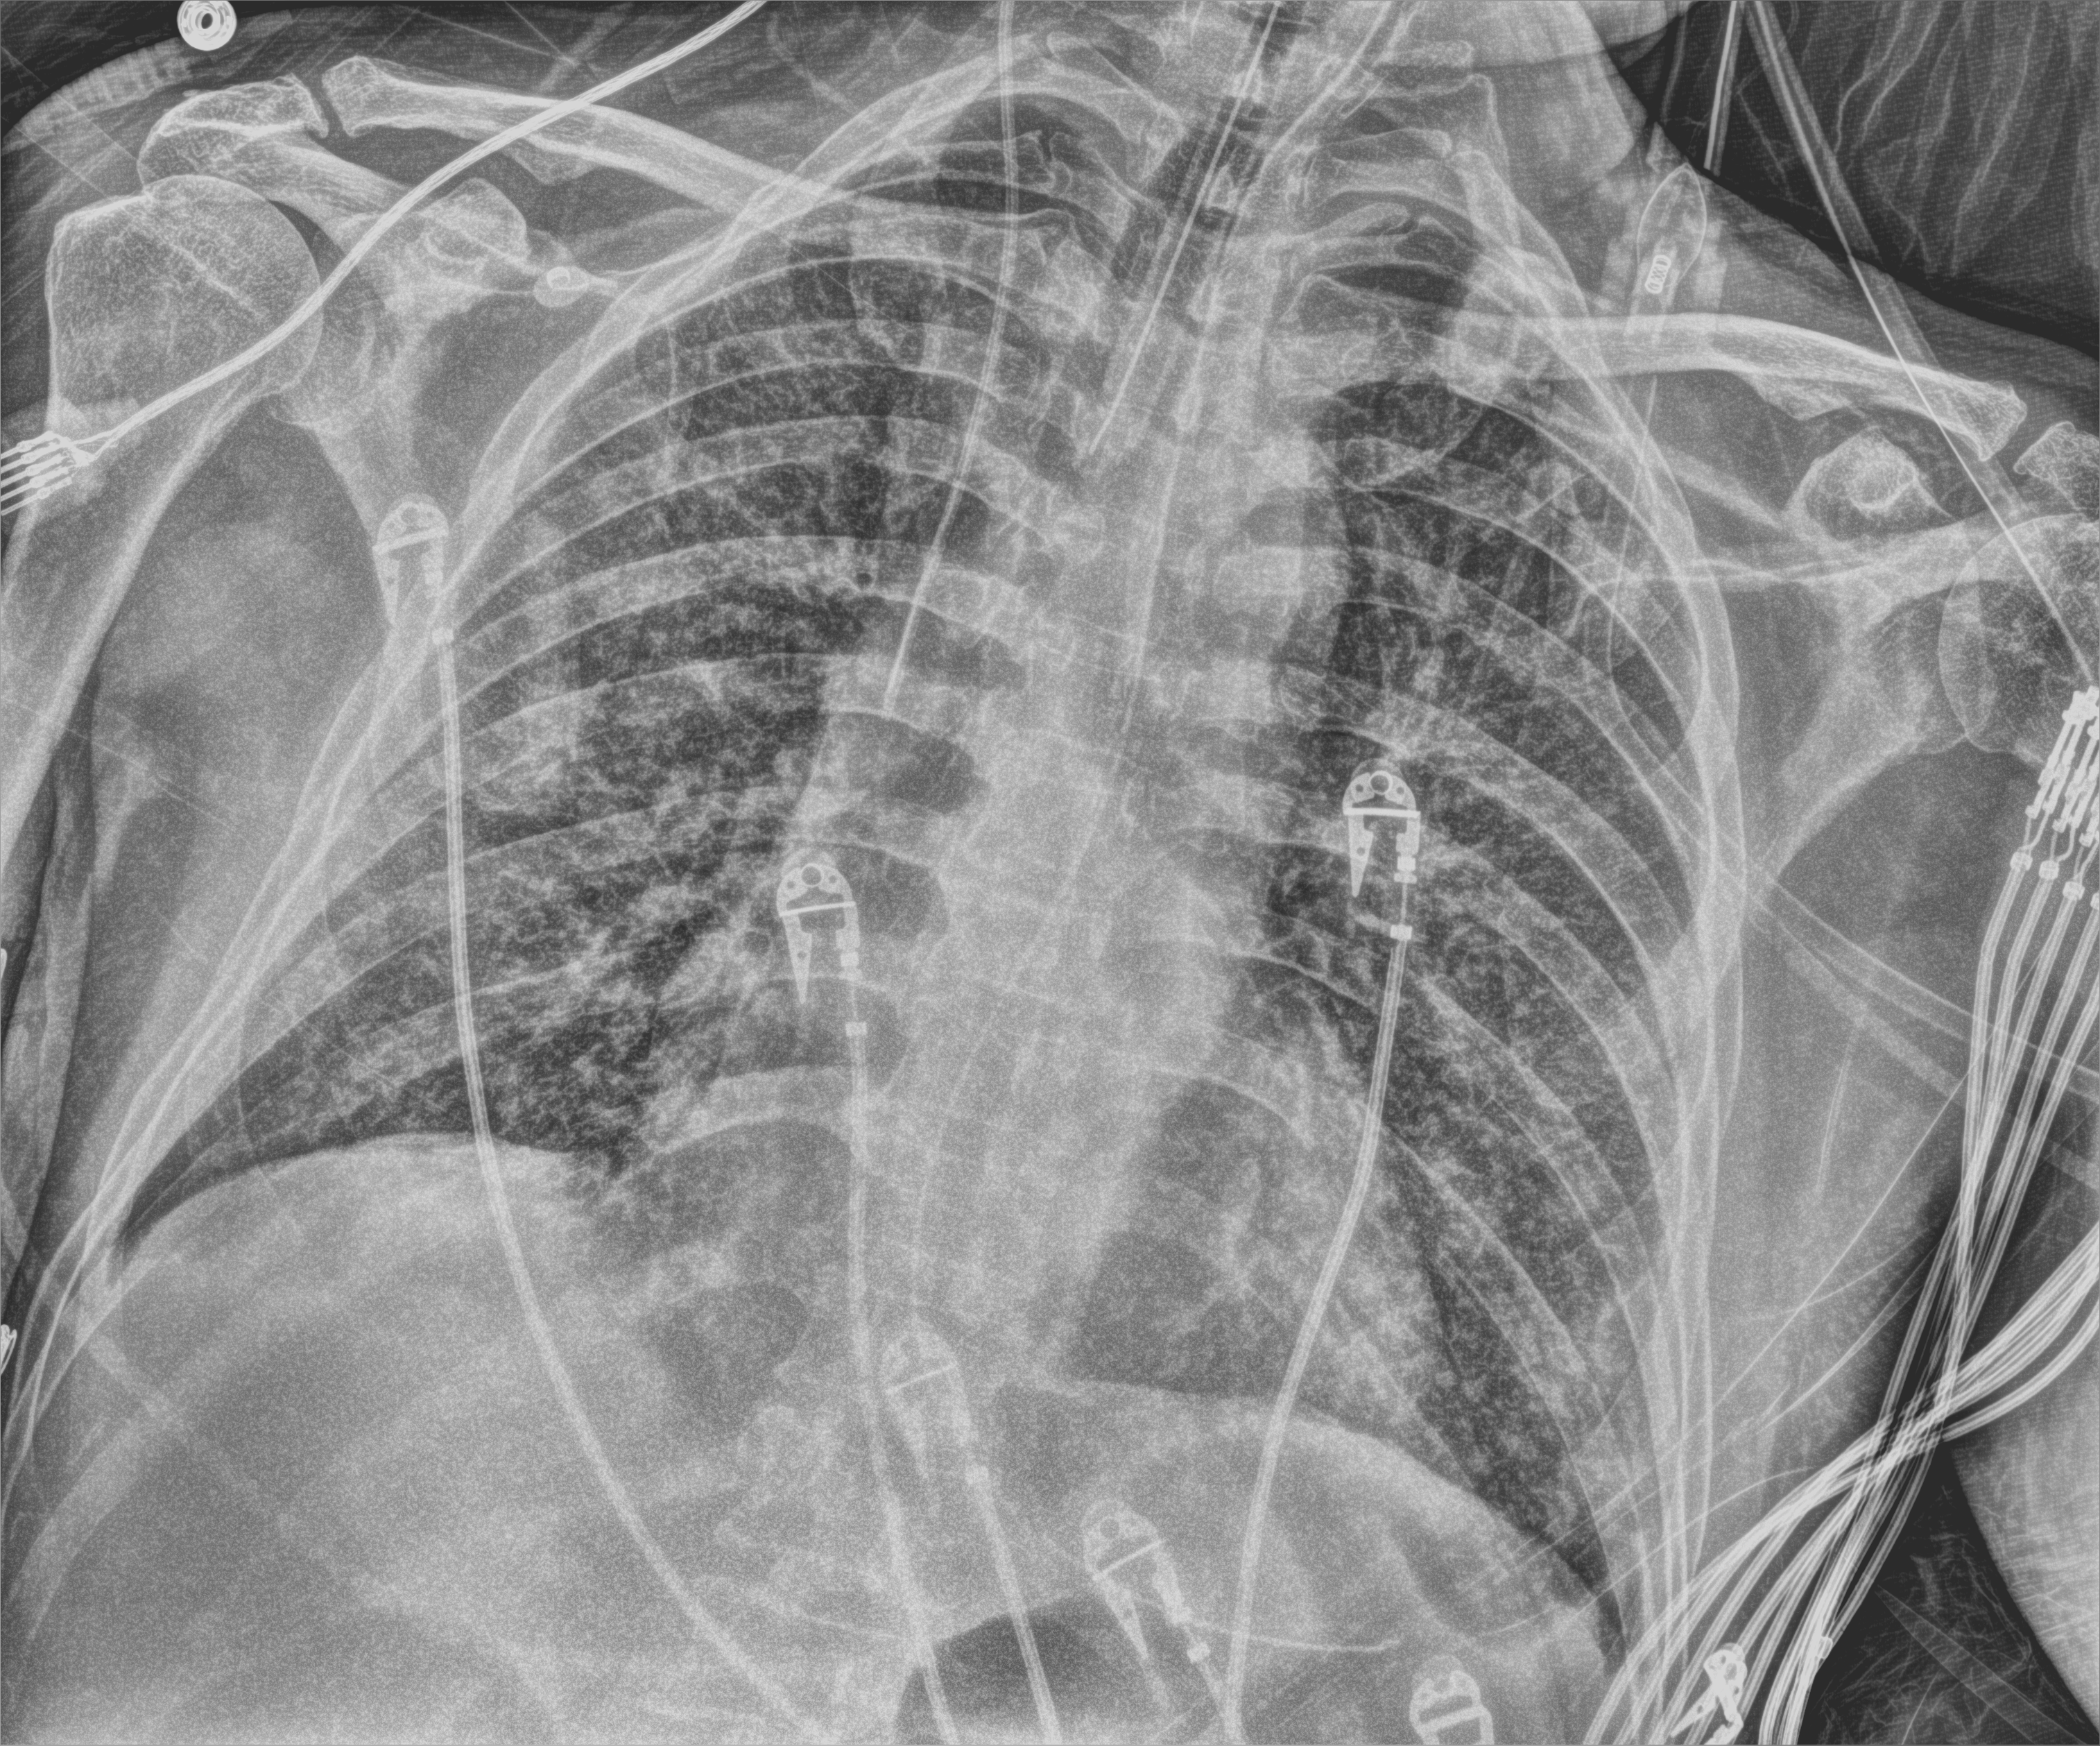
Portable chest radiograph, anteroposterior (AP) projection. Male patient hospitalised with COVID-19, age 60–74 years.
Admission-level facts for this patient (not findings on this image; timing relative to this image not recorded): admitted to intensive care during this hospital stay: yes.